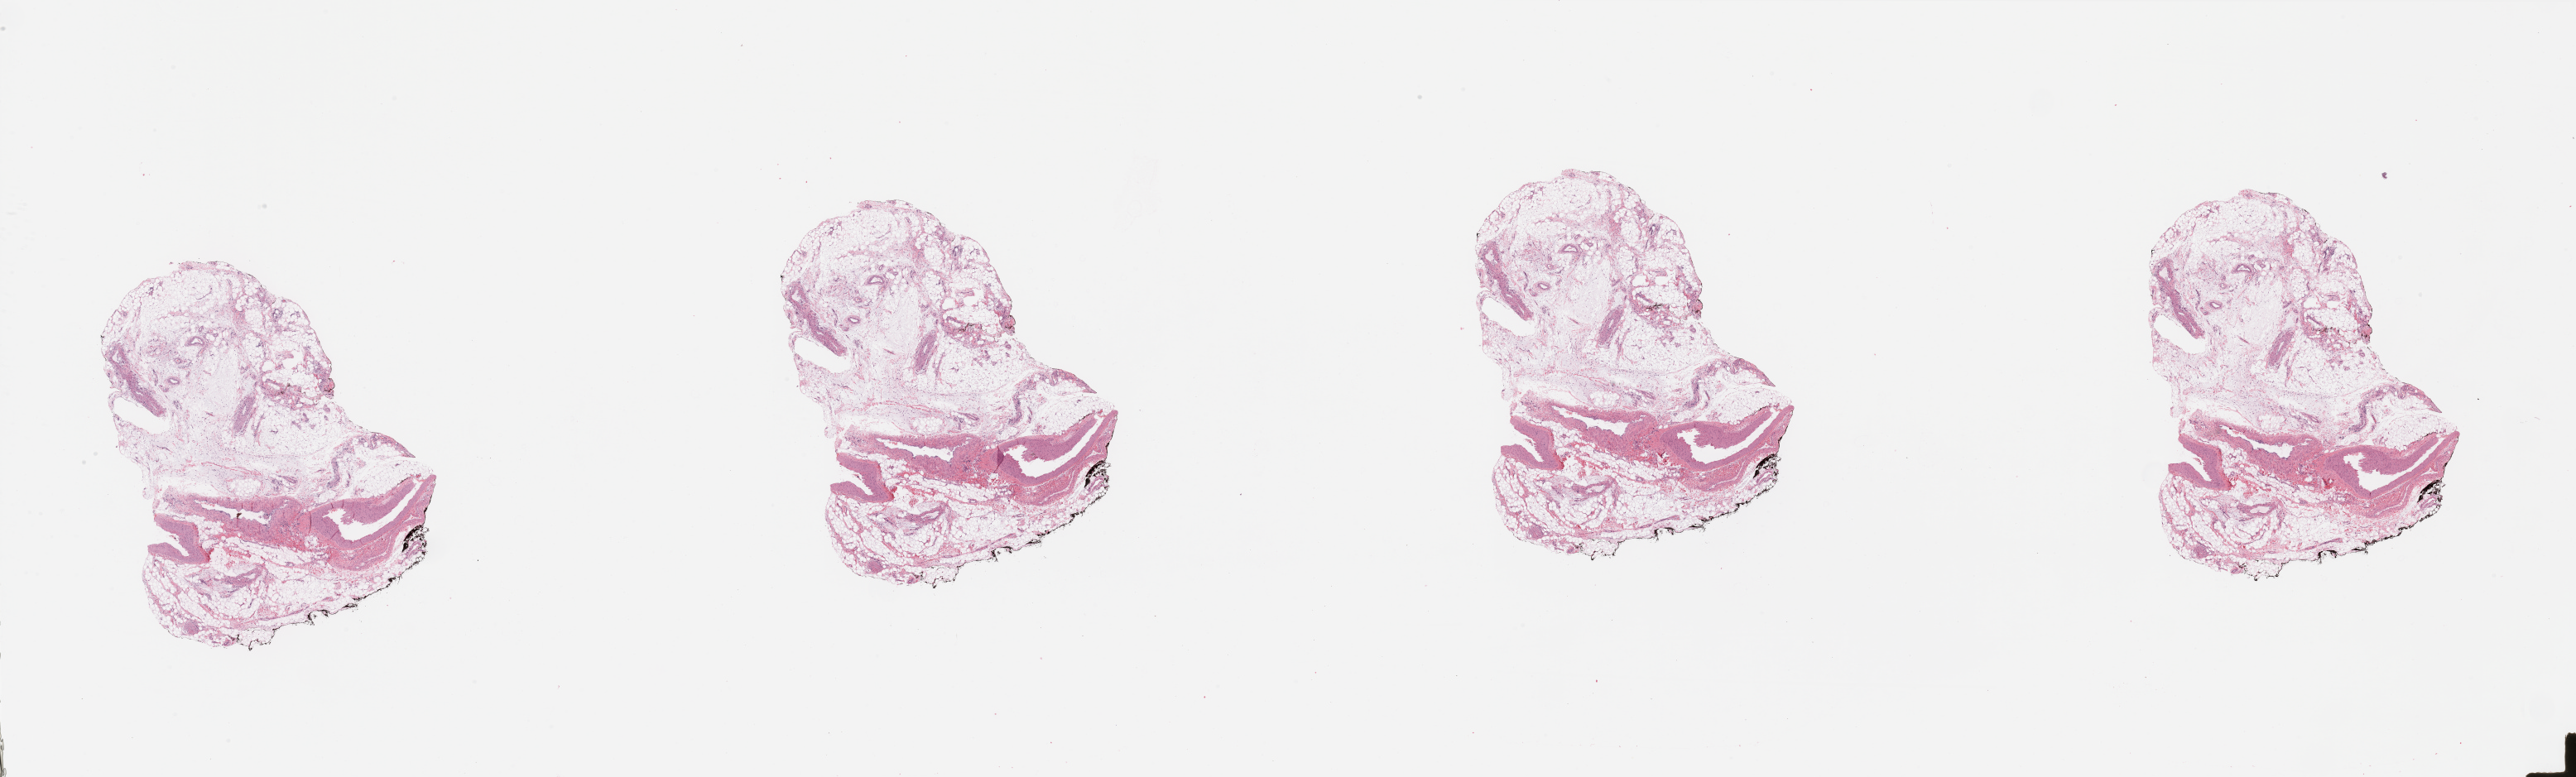
Digitized H&E-stained tissue section (whole slide), whole scanned area (about 49.2 x 14.9 mm) shown as a low-resolution overview. Pancreas, normal (non-tumour) tissue. Patient: female, age 74 years.
This section: normal (non-tumour) tissue from the same patient. Patient diagnosis (cohort enrolment): ductal adenocarcinoma (pancreas).